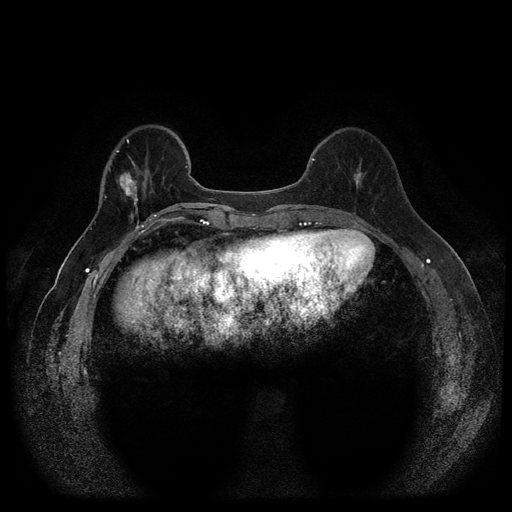
Breast MRI (dynamic contrast-enhanced, multi-phase), one axial slice. Position 31 of 116 along the scan axis. Dynamic contrast-enhanced series, time point 2 of 5 at this slice position (early post-contrast). 1.5 T. TE 2.6 ms, TR 5.4 ms. 2 mm slice thickness. 512 × 512 image matrix, field of view 340 × 340 mm. Patient: female, 56 years.
Structures marked on this image (semi-automatically segmented with operator editing):
- breast lesion (labelled 'tumour' in the annotation; benign lesions carry a separate 'benign' label): bounding box <116,164,152,221> (left, top, right, bottom; pixels)